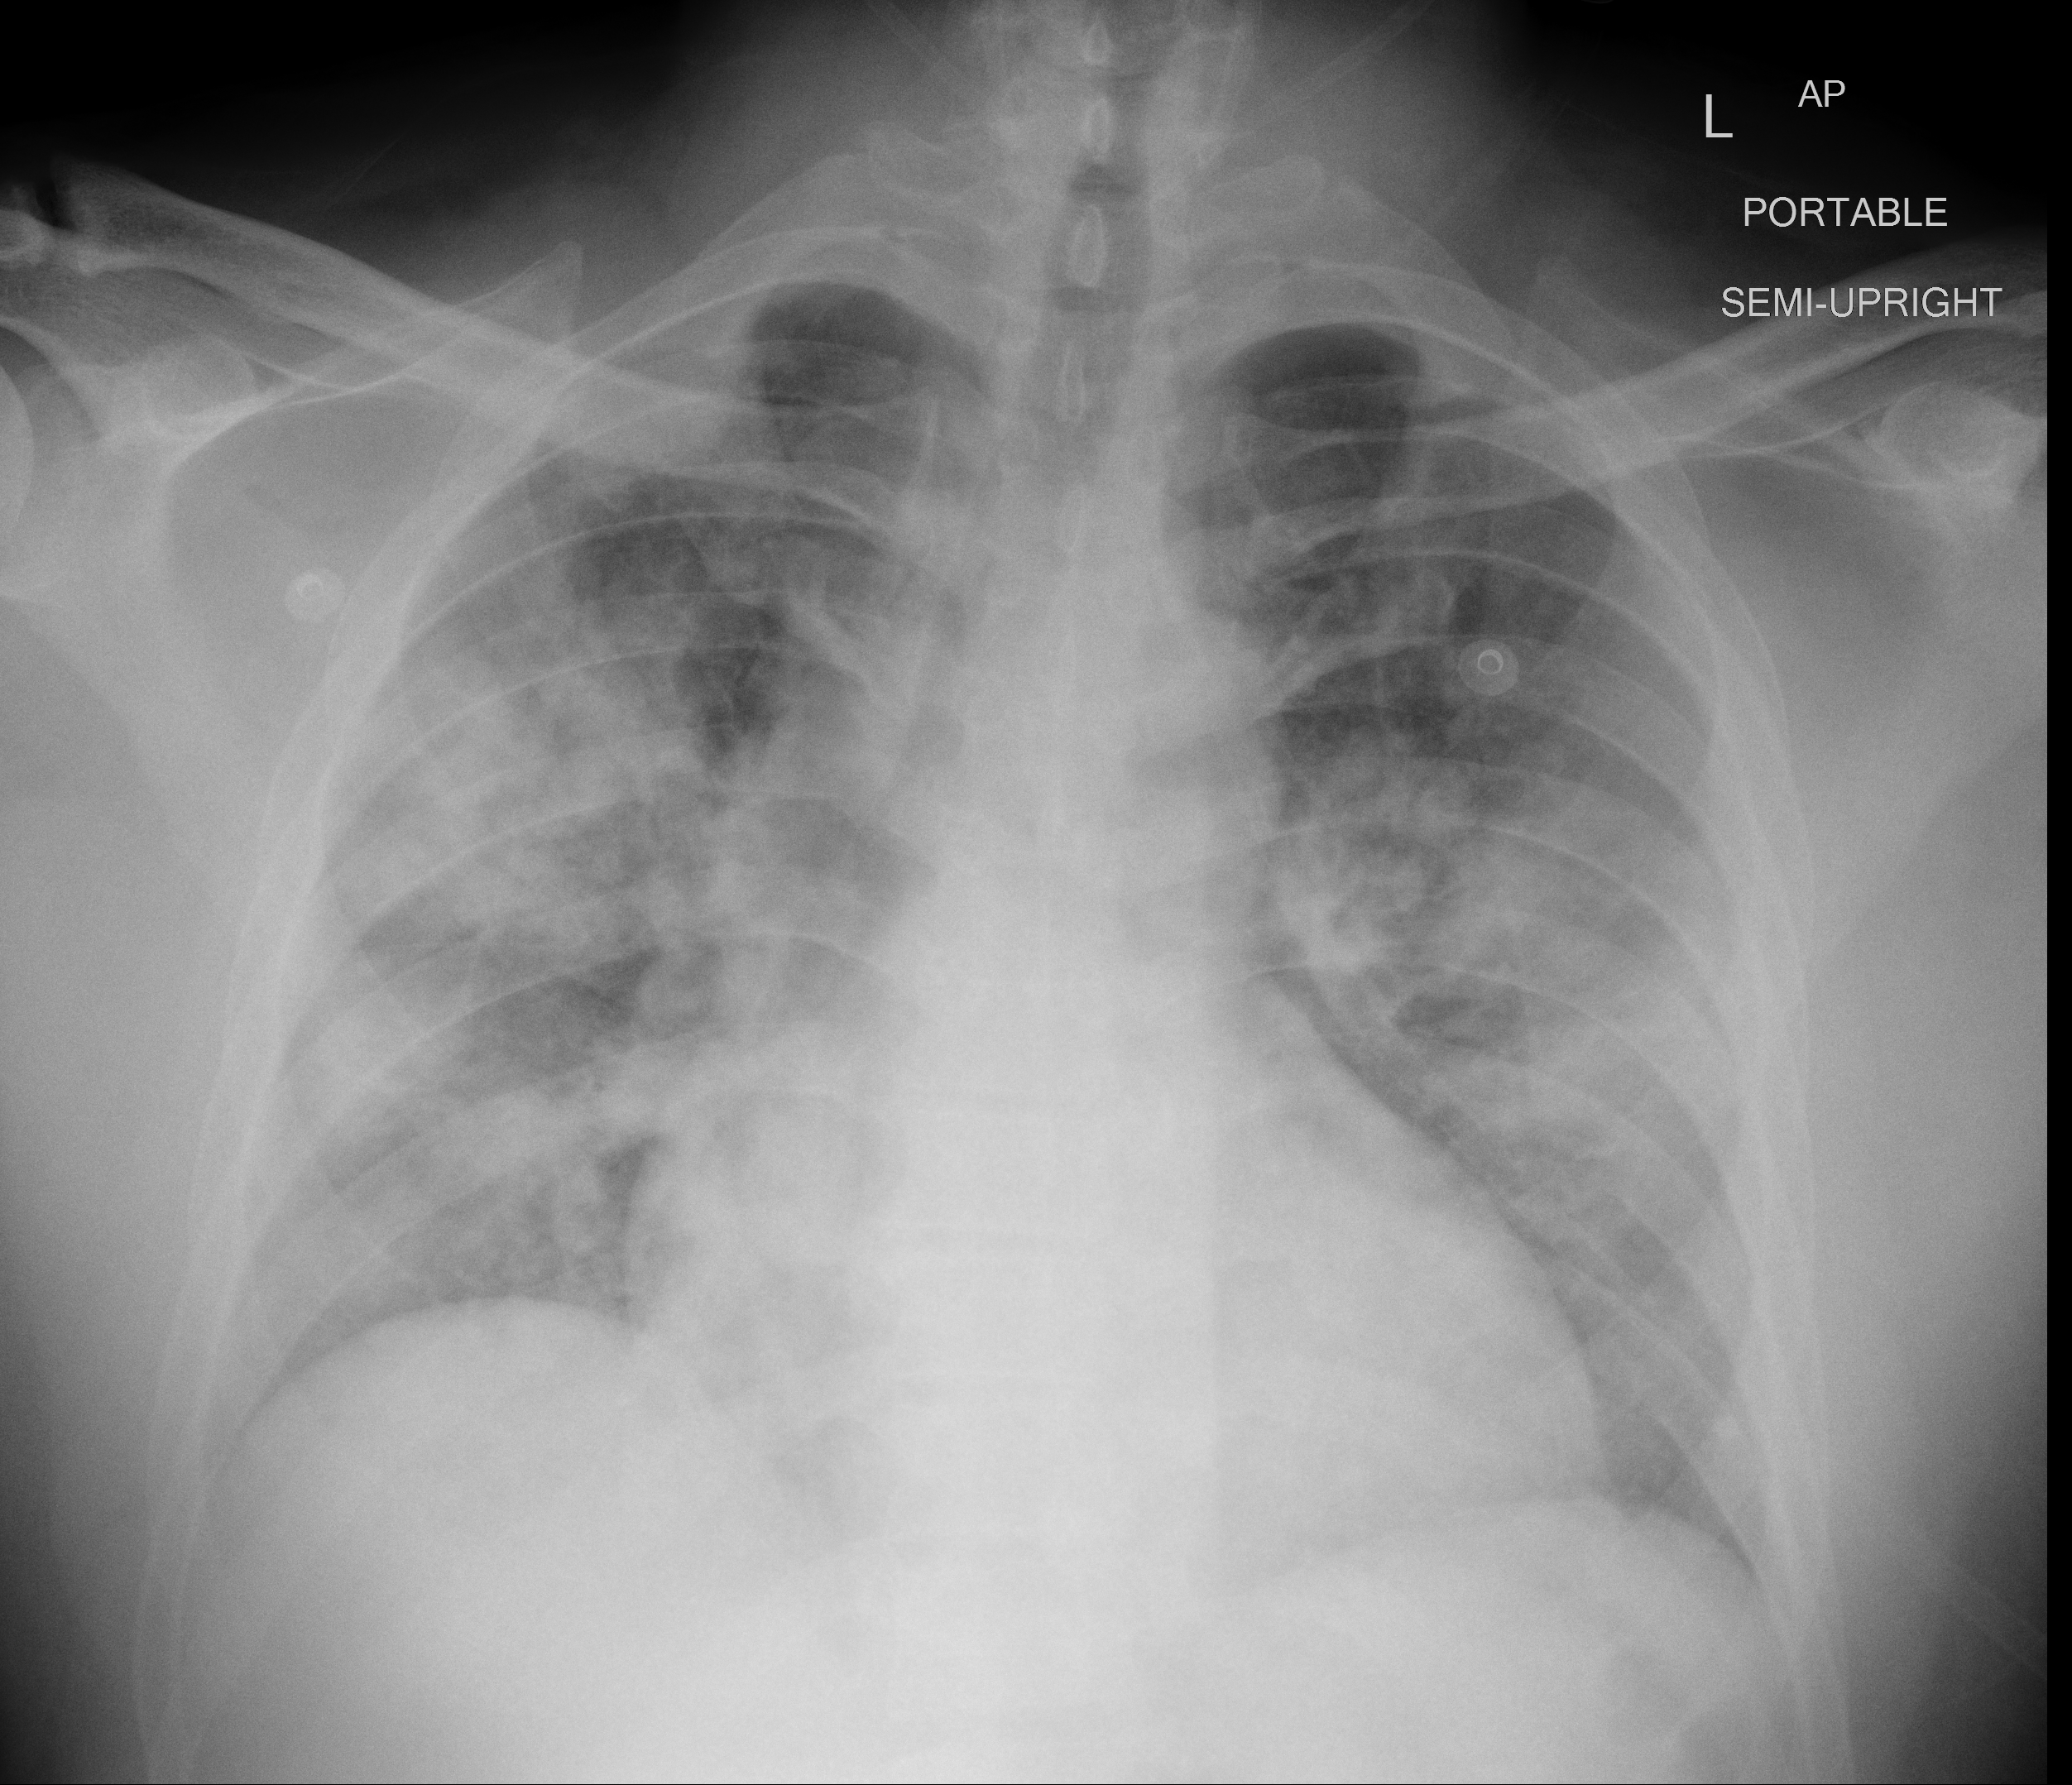
Portable chest radiograph, AP projection. Male patient, age 48 years; imaged 2 days after the COVID-19 diagnosis.
Key findings recorded by the radiologist: significant worsening of airspace disease, now very extensive and patchy sparing only apices.